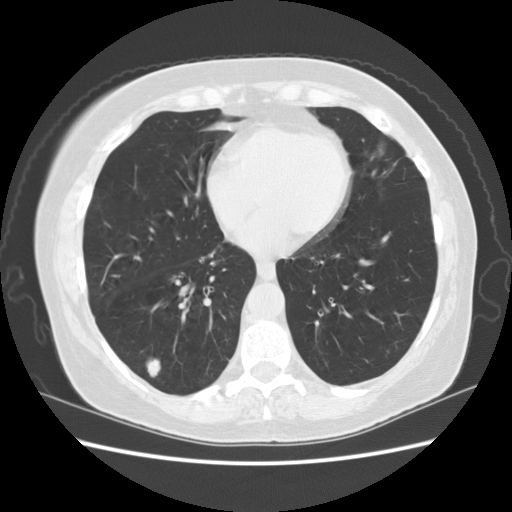
Low-dose screening chest CT, one axial slice; slice 52 of 156 in the series (ordered by position); reconstruction kernel STANDARD; 120 kVp; lung window (W 1500 / L -600 HU); 512 × 512 image matrix, field of view 360 × 360 mm.
Annotated regions visible in this slice (outlined manually by an expert reader):
- lesion 1 (tumor, lower lobe of right lung): bounding box <148,360,160,377> (left, top, right, bottom; pixels)